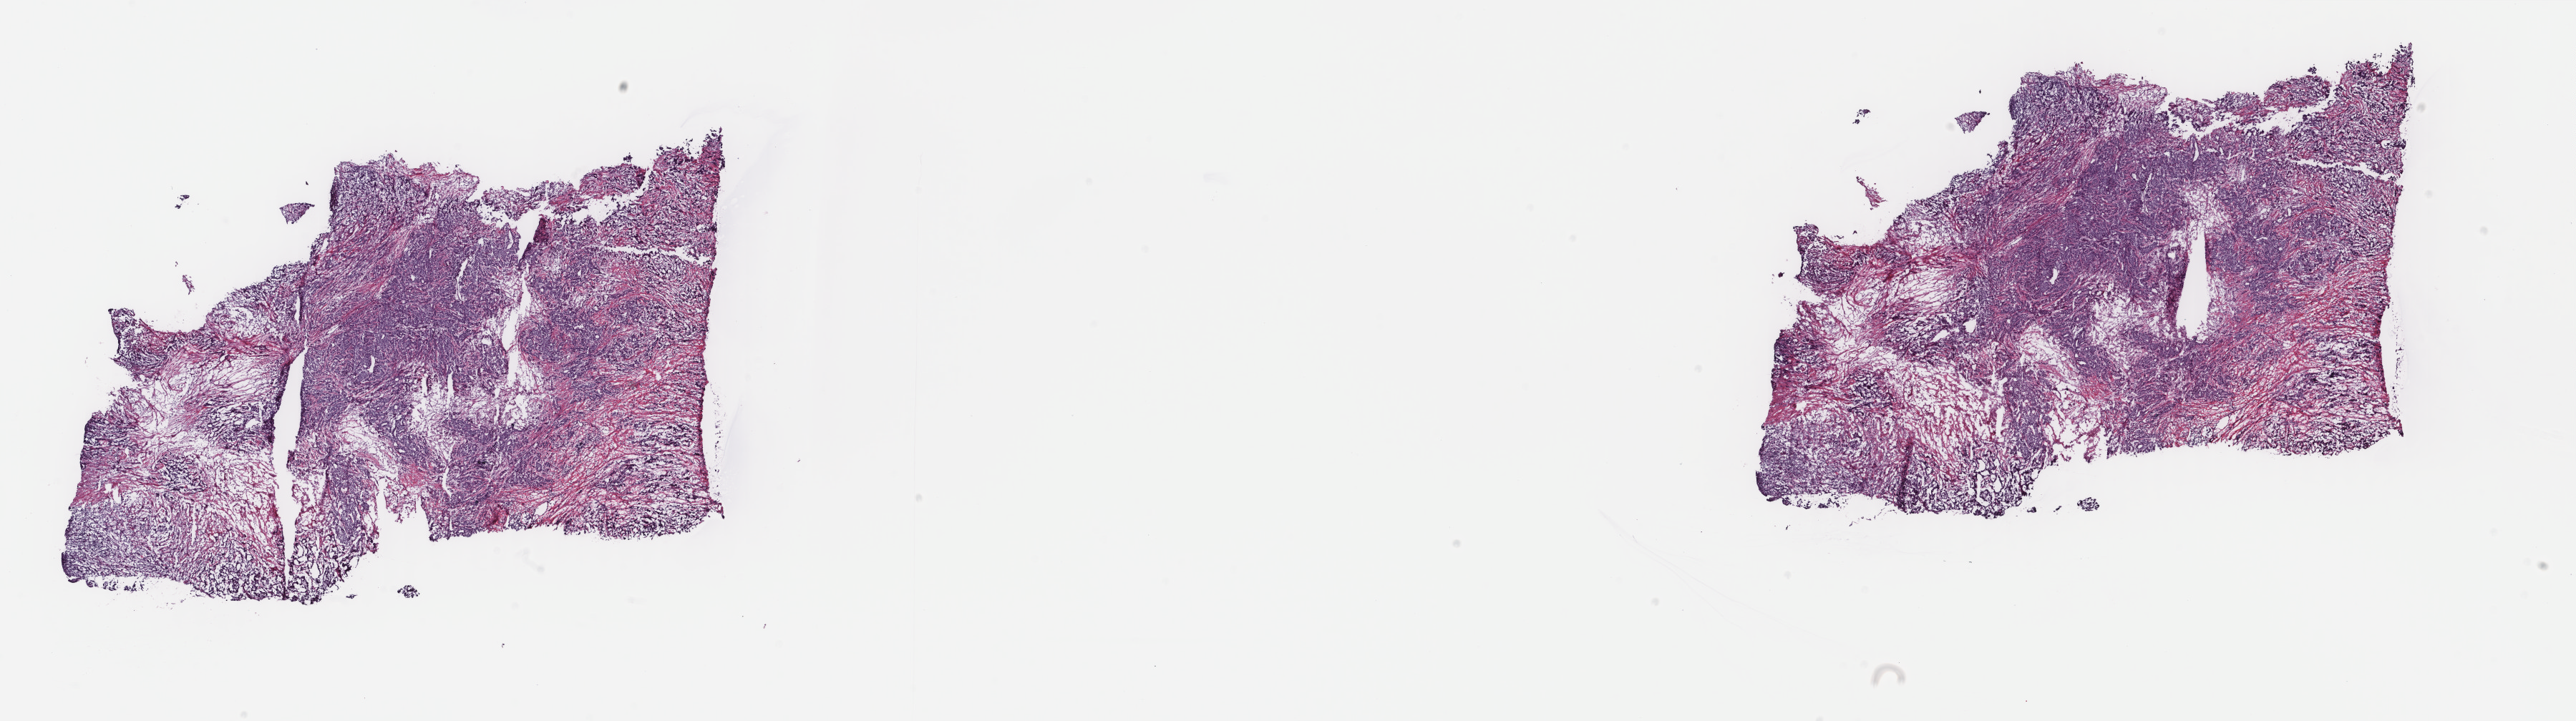
Whole-slide histology image, H&E — whole scanned area (about 28.6 x 8.0 mm, slide scanned at 40x) shown as a low-resolution overview. Frozen section from the top of the tissue portion. Primary tumour sample from the breast. Female, age 77 years at initial diagnosis. Pathologist review of this section (percent, as recorded): tumour cells 100%, tumour nuclei 90%, normal cells 0%, stromal cells 0%, necrosis 0%. Inflammatory infiltration, as recorded: lymphocyte infiltration 0%, monocyte infiltration 0%, neutrophil infiltration 0%.
AJCC pathologic stage: IIB (7th edition). Lymph nodes positive (case pathology): 3 of 16 examined. Diagnosis: Infiltrating duct carcinoma, NOS.